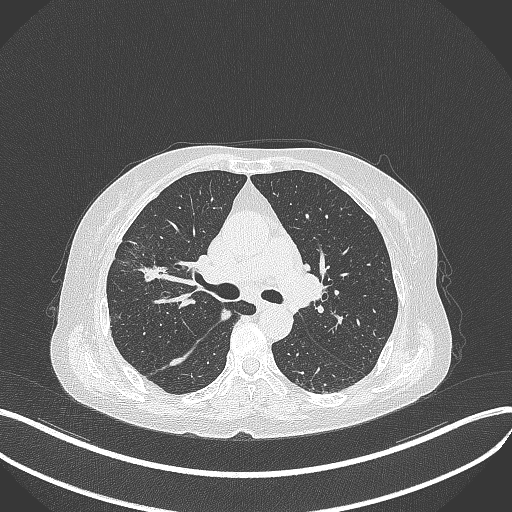
Chest CT, one axial slice. Slice 251 of 429 in the series (ordered by position). Reconstruction kernel B70f. Lung window (W 1500 / L -600 HU). 1 mm slice thickness. 512 × 512 image matrix, field of view 400 × 400 mm. Female patient, age 69 years. Case-level facts recorded for this patient, not image findings: clinical TNM (as recorded): T1b N3 M0.
Outlined on this slice (bounding box drawn by a radiologist):
- lung tumour (recorded histology: small cell carcinoma): bounding box (x1, y1, x2, y2) in pixels: (128, 257, 177, 286)